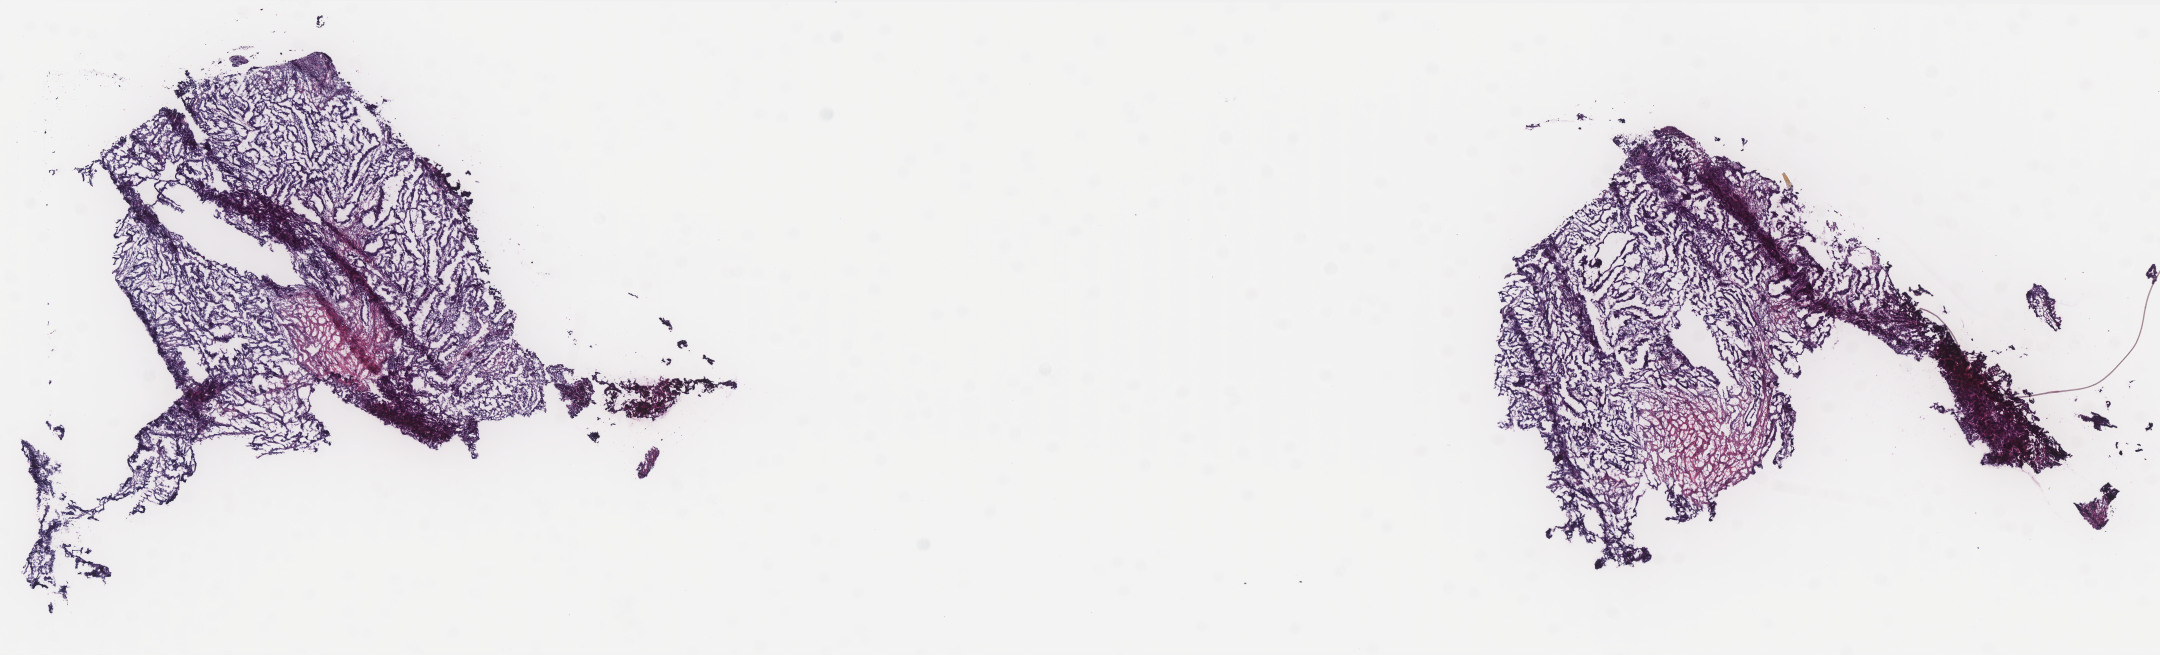
Whole-slide histology image, H&E — shown as a low-resolution overview of the whole scanned area (about 17.3 x 5.3 mm, acquisition: 40x scan); frozen section from the bottom of the tissue portion; primary tumour sample from the uterus. Patient: female, age at initial diagnosis 64 years. Histologic grade: G2 (moderately differentiated). Slide review estimates, as recorded: tumour cells 70%, tumour nuclei 70%, normal cells 20%, stromal cells 0%, necrosis 10%. Infiltration values recorded for this section: lymphocyte infiltration 20%, monocyte infiltration 0%, neutrophil infiltration 20%.
FIGO stage: IB. Diagnosis: Endometrioid adenocarcinoma, NOS.